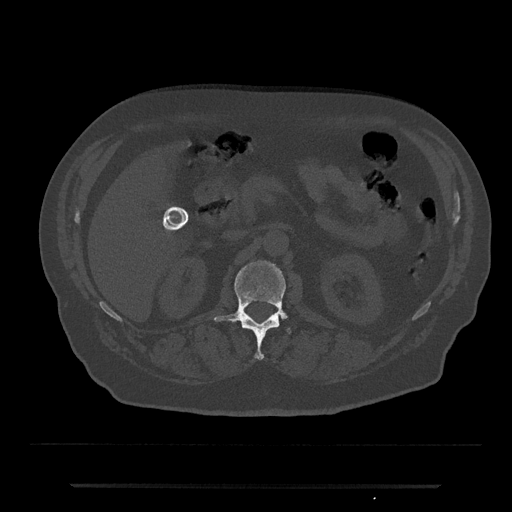
CT including the spine, one axial slice. Position 531 of 797 along the scan axis. Reconstruction kernel Br40s/3. Bone window (W 1800 / L 400 HU). 512 × 512 image matrix, field of view 434 × 434 mm. Patient: male, 80 years. Case-level facts recorded for this patient, not image findings: primary cancer: prostate.
Outlined on this slice (semi-automatically segmented with operator editing):
- L1 vertebra: bounding box <215,260,290,360> (left, top, right, bottom; pixels)